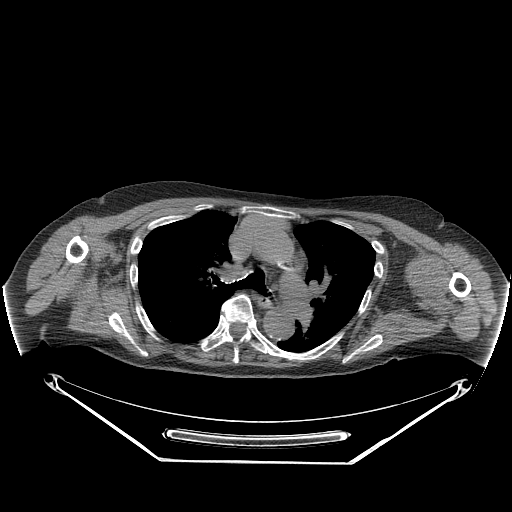
CT of an extremity soft-tissue mass (from a PET/CT study), one axial slice; position 185 of 267 along the scan axis; reconstruction kernel STANDARD; soft-tissue window (W 400 / L 40 HU); 3.75 mm slice thickness; 512 × 512 image matrix. Female patient. Case-level facts recorded for this patient, not image findings: histological type: pleiomorphic leiomyosarcoma; grade: high; site of the primary tumour: left biceps.
Outlined on this slice (expert contour drawn on MRI and transferred to this co-registered scan by the dataset authors):
- gross tumour volume including surrounding oedema: bounding box <411,256,442,305> (left, top, right, bottom; pixels)
- gross tumour volume (mass): <413,260,439,286>